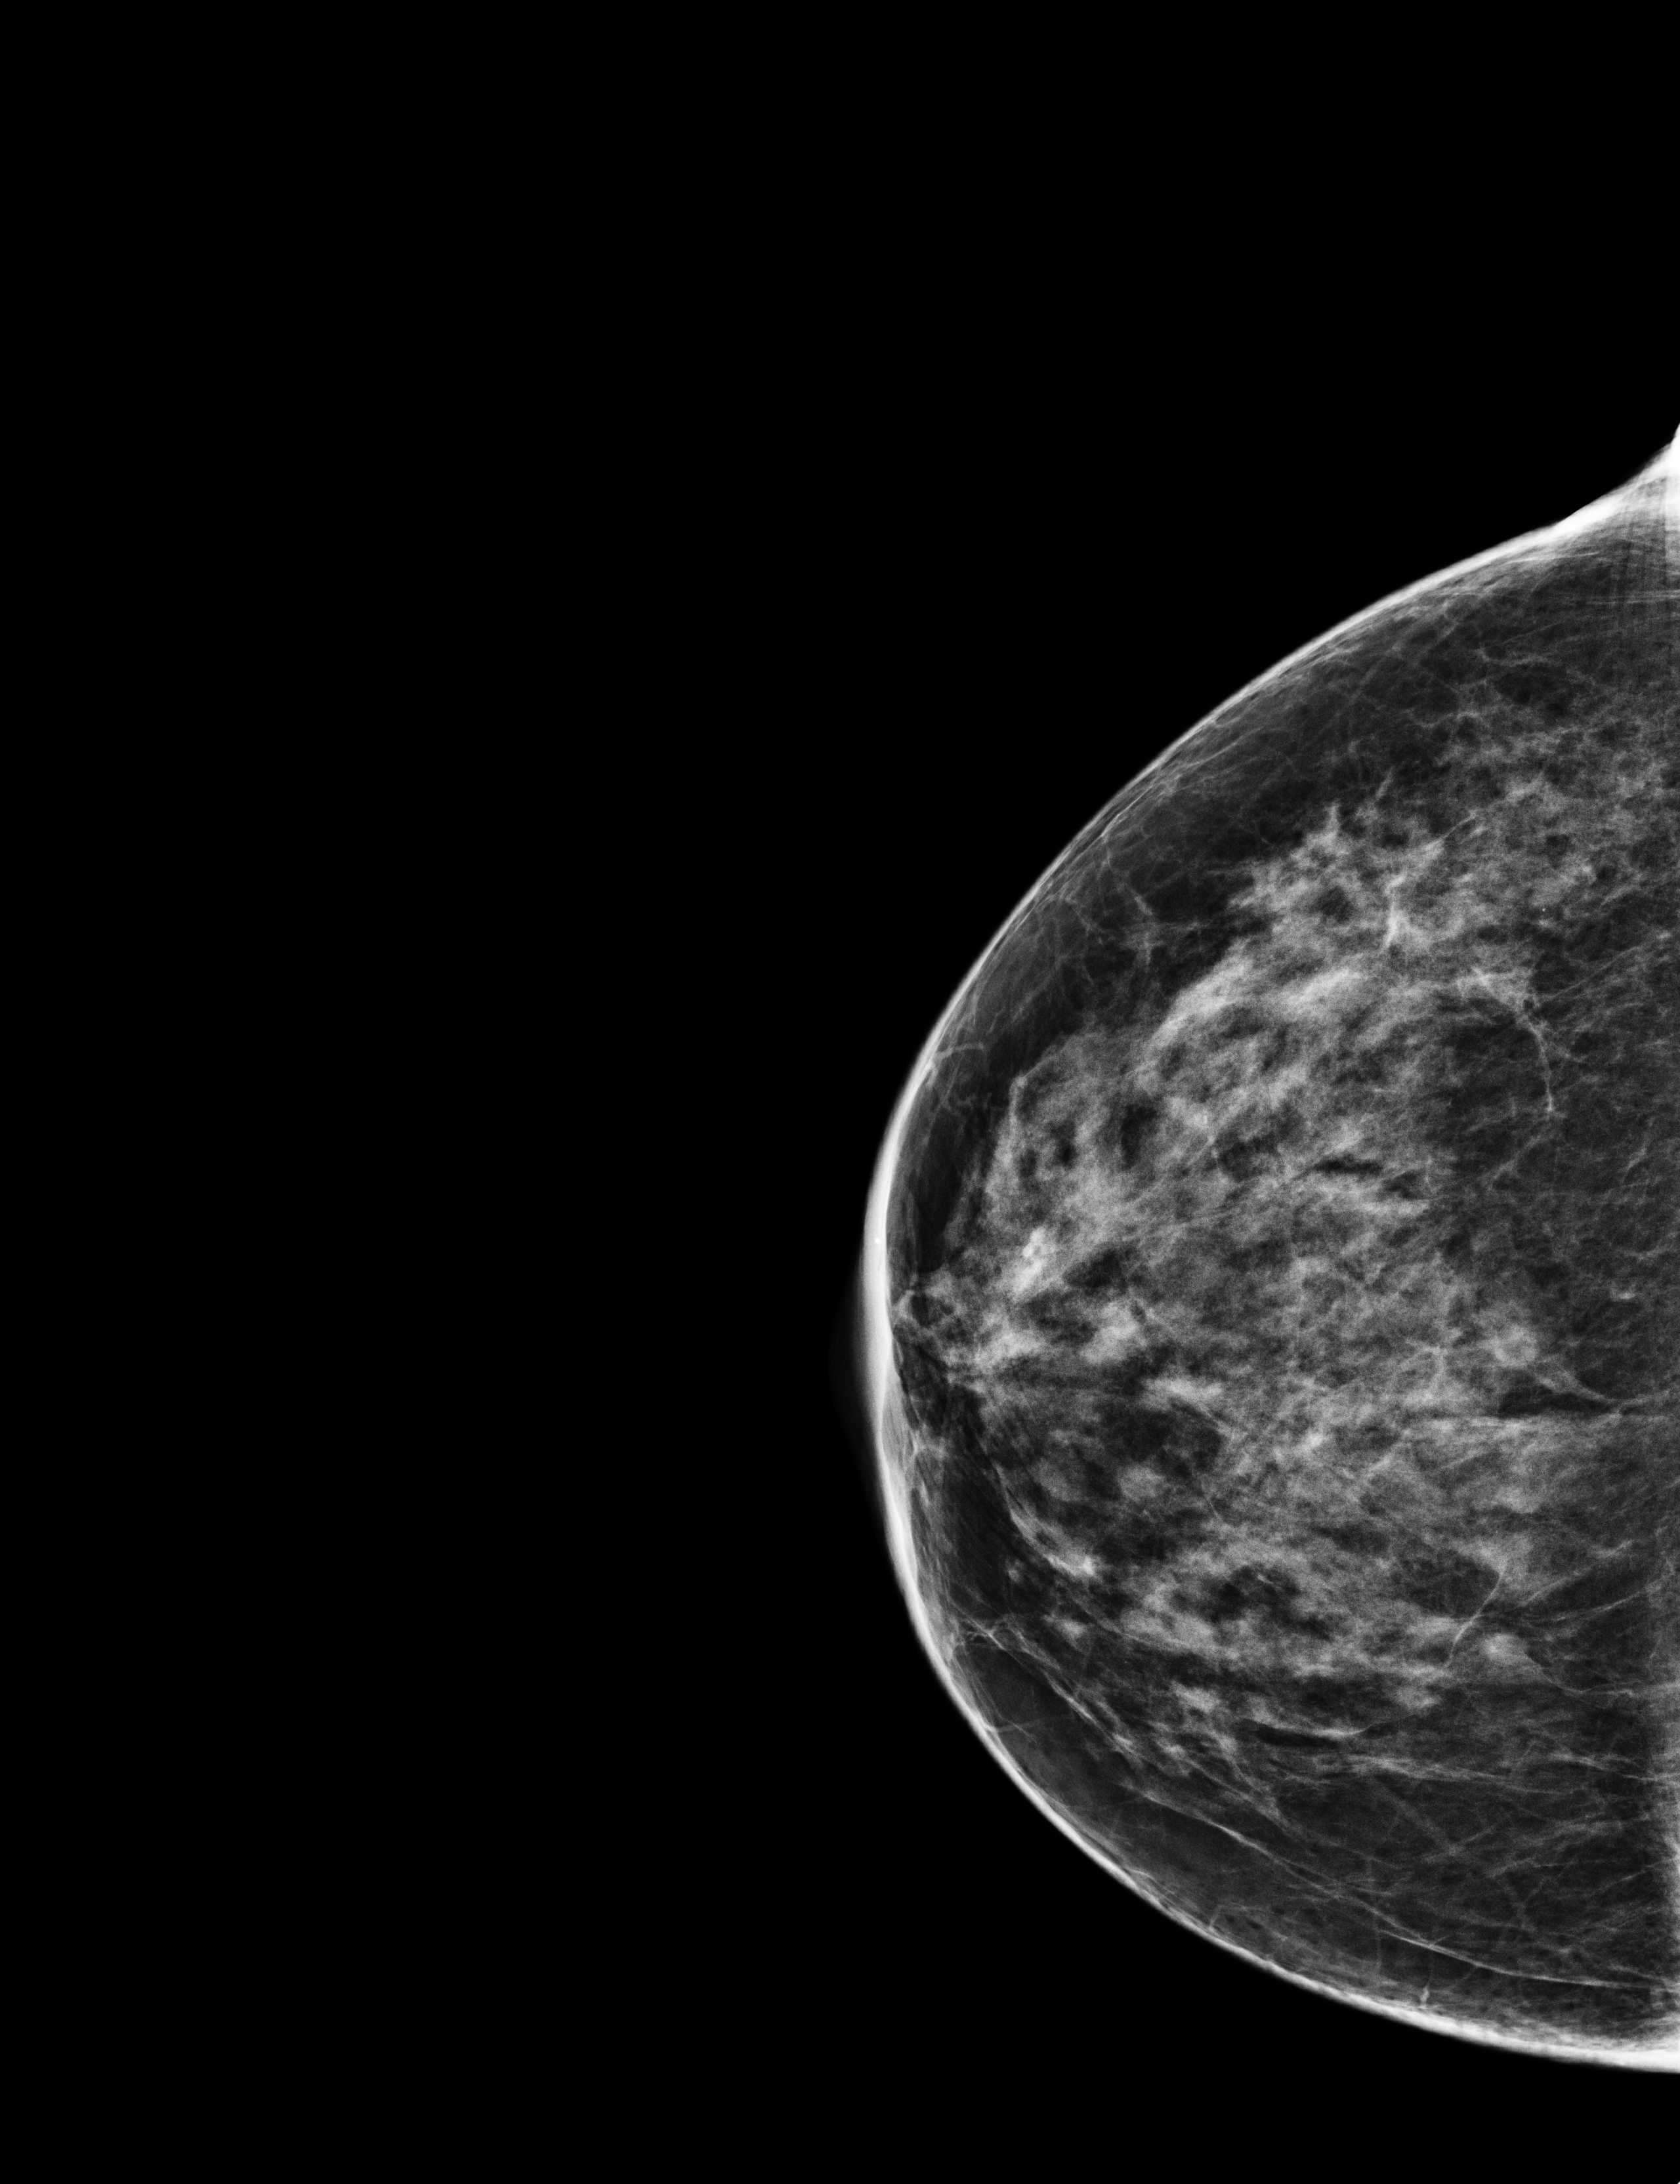
Annual screening mammography examination. Patient: female, 61 years.
Image type: full-field digital mammogram. Breast: right. Projection: CC view.